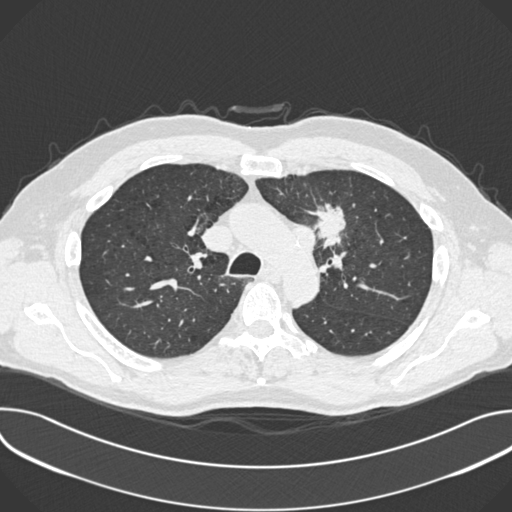
Low-dose screening chest CT, one axial slice. Position 264 of 361 along the scan axis. Reconstruction kernel B30f. Lung window (W 1500 / L -600 HU). 1 mm slice thickness. 512 × 512 image matrix, field of view 380 × 380 mm.
Annotated regions visible in this slice (outlined manually by an expert reader):
- lesion 1 (tumor, upper lobe of left lung): bounding box [x1, y1, x2, y2] px = [313, 207, 346, 247]